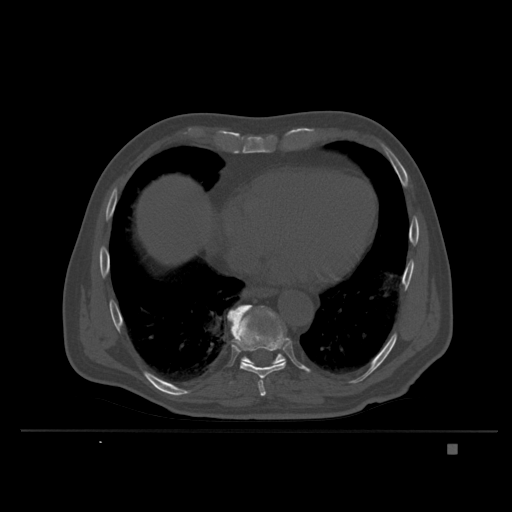
CT including the spine, one axial slice. Slice 208 of 435 in the series (ordered by position). Bone window (W 1800 / L 400 HU). 512 × 512 image matrix, field of view 434 × 434 mm. Male patient, age 73 years. Case-level facts recorded for this patient, not image findings: primary cancer: skin.
Structures marked on this image (semi-automatic segmentation, software-assisted and operator-edited):
- T10 vertebra: box from (x=241, y=307) to (x=285, y=366) px
- T9 vertebra: (x=227, y=304)–(x=289, y=397)